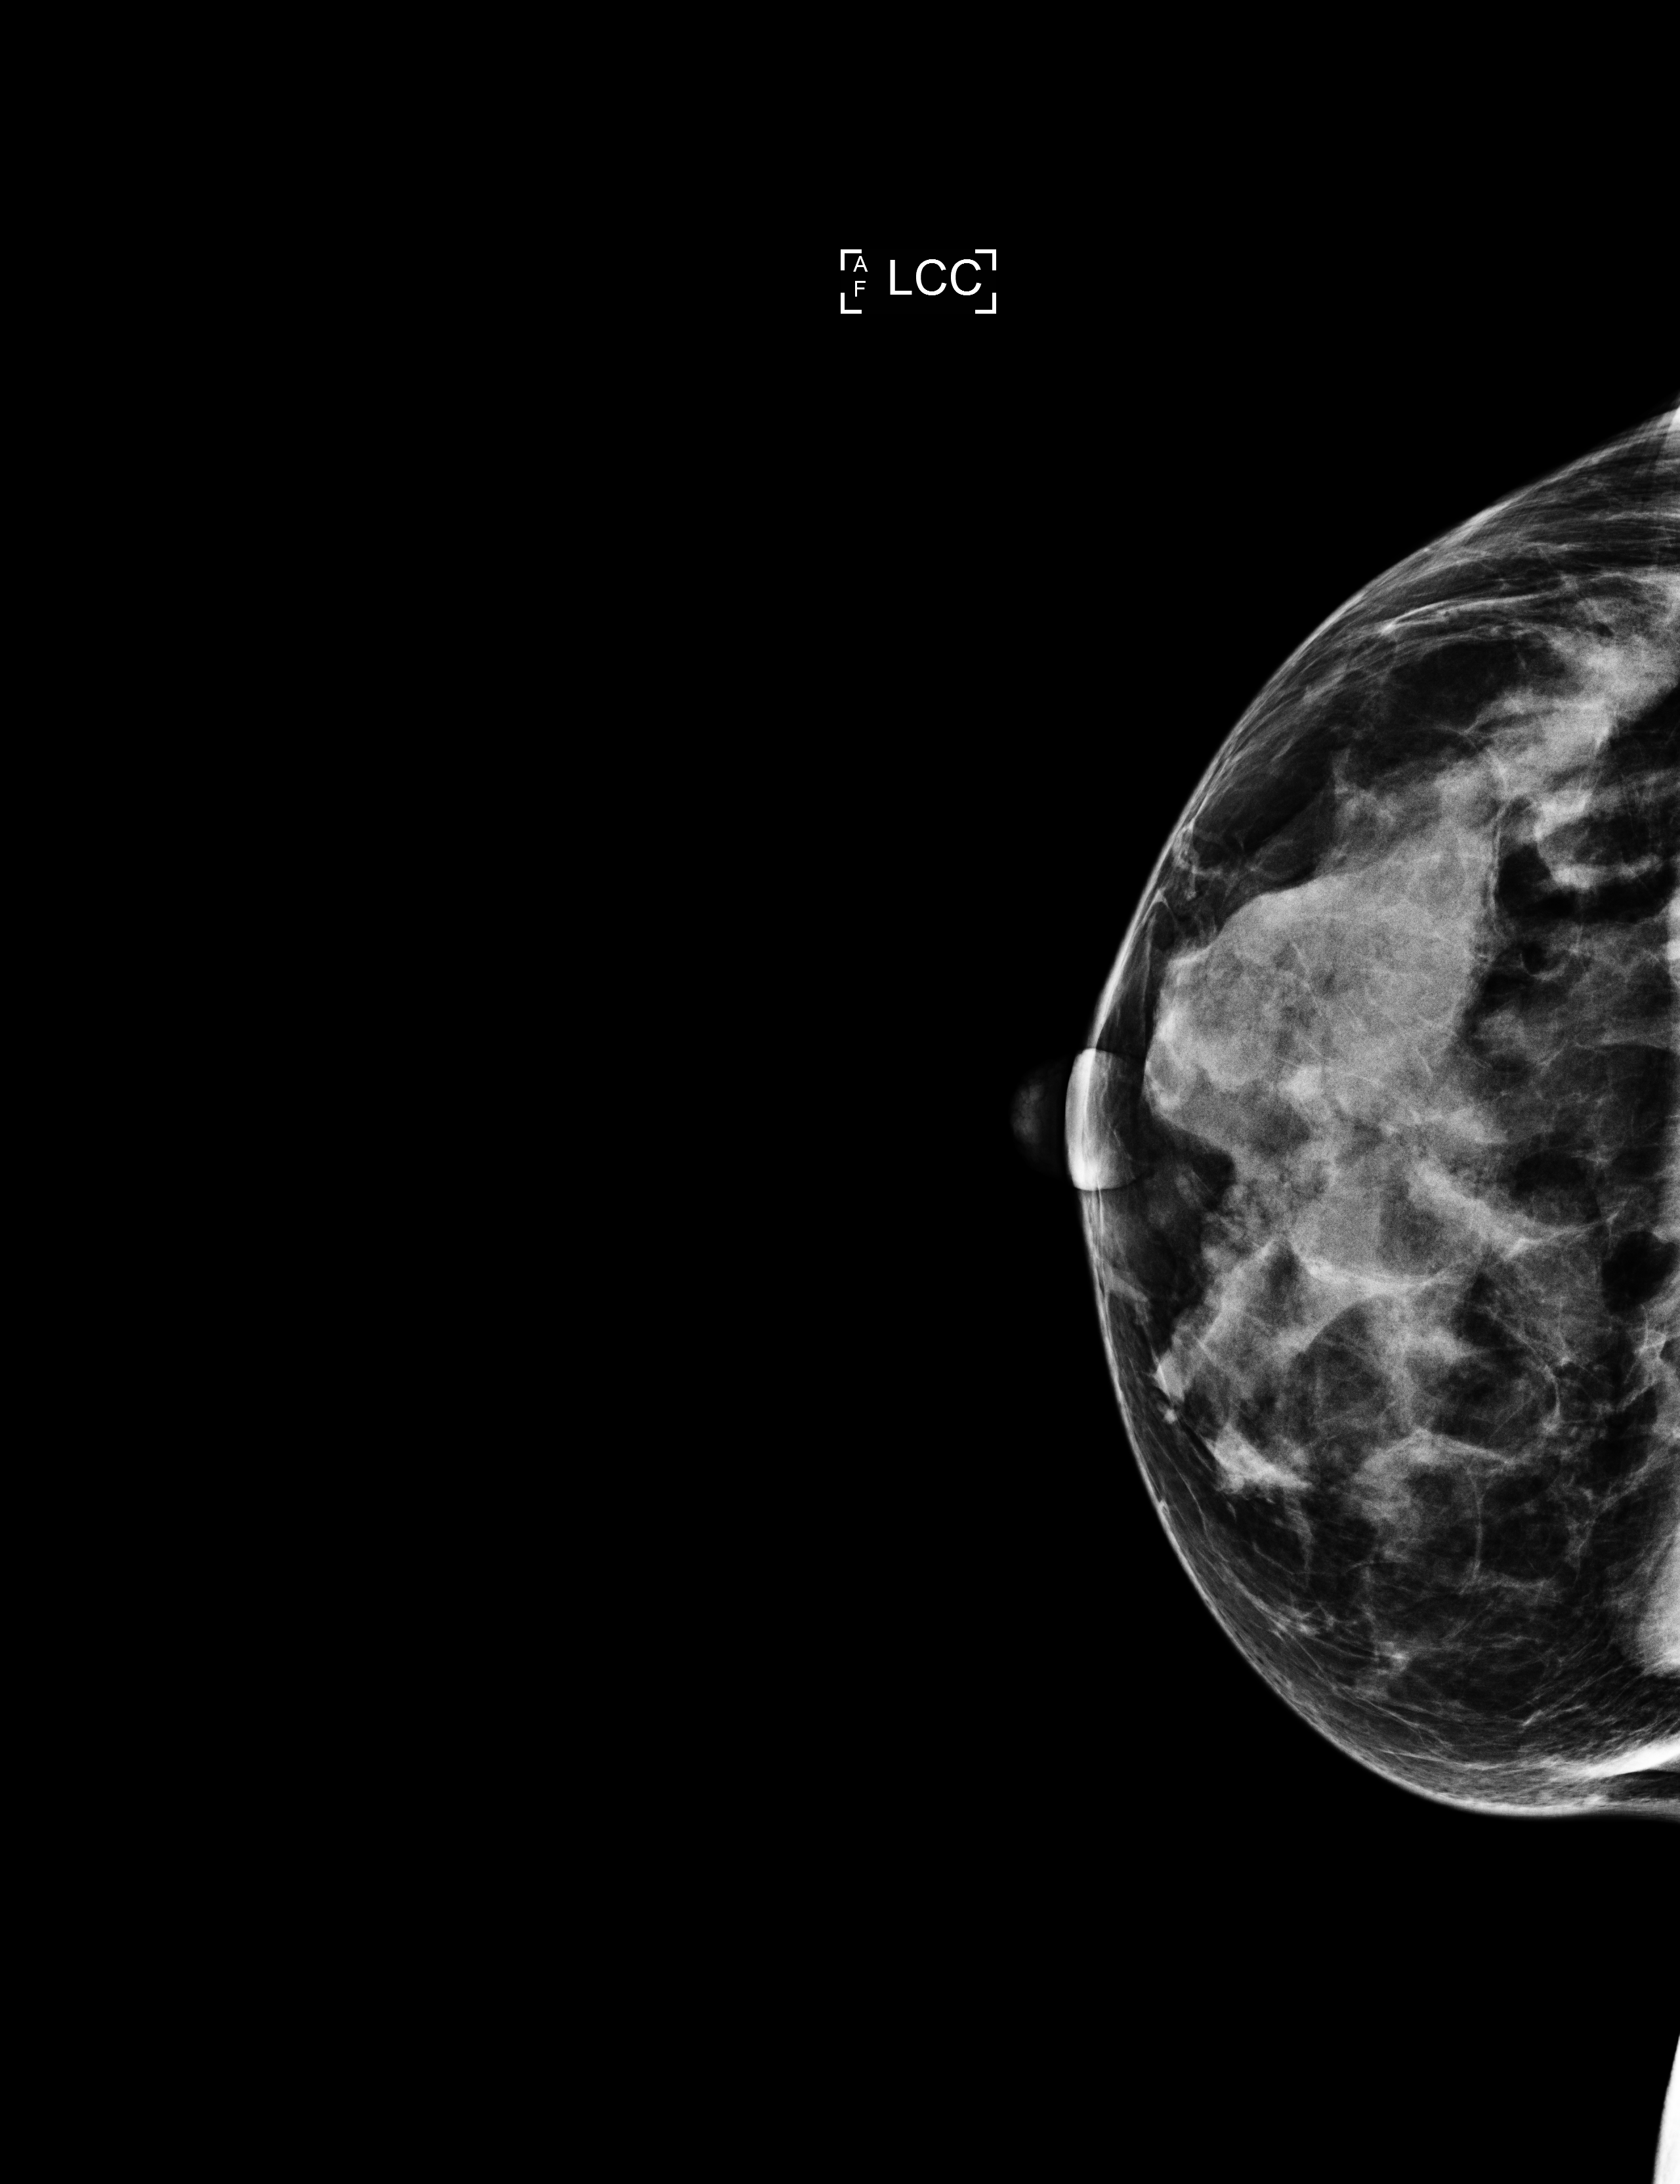
Full-field digital mammogram (FFDM), left breast, CC view, annual screening mammography examination, compressed breast thickness 33 mm. Patient aged 53 years (female).
Breast density at the screening exam (both breasts): heterogeneously dense (BI-RADS density category c). Final BI-RADS assessment for this screening round (tomosynthesis exam, both breasts): category 1. Recall: no recall after this screen.